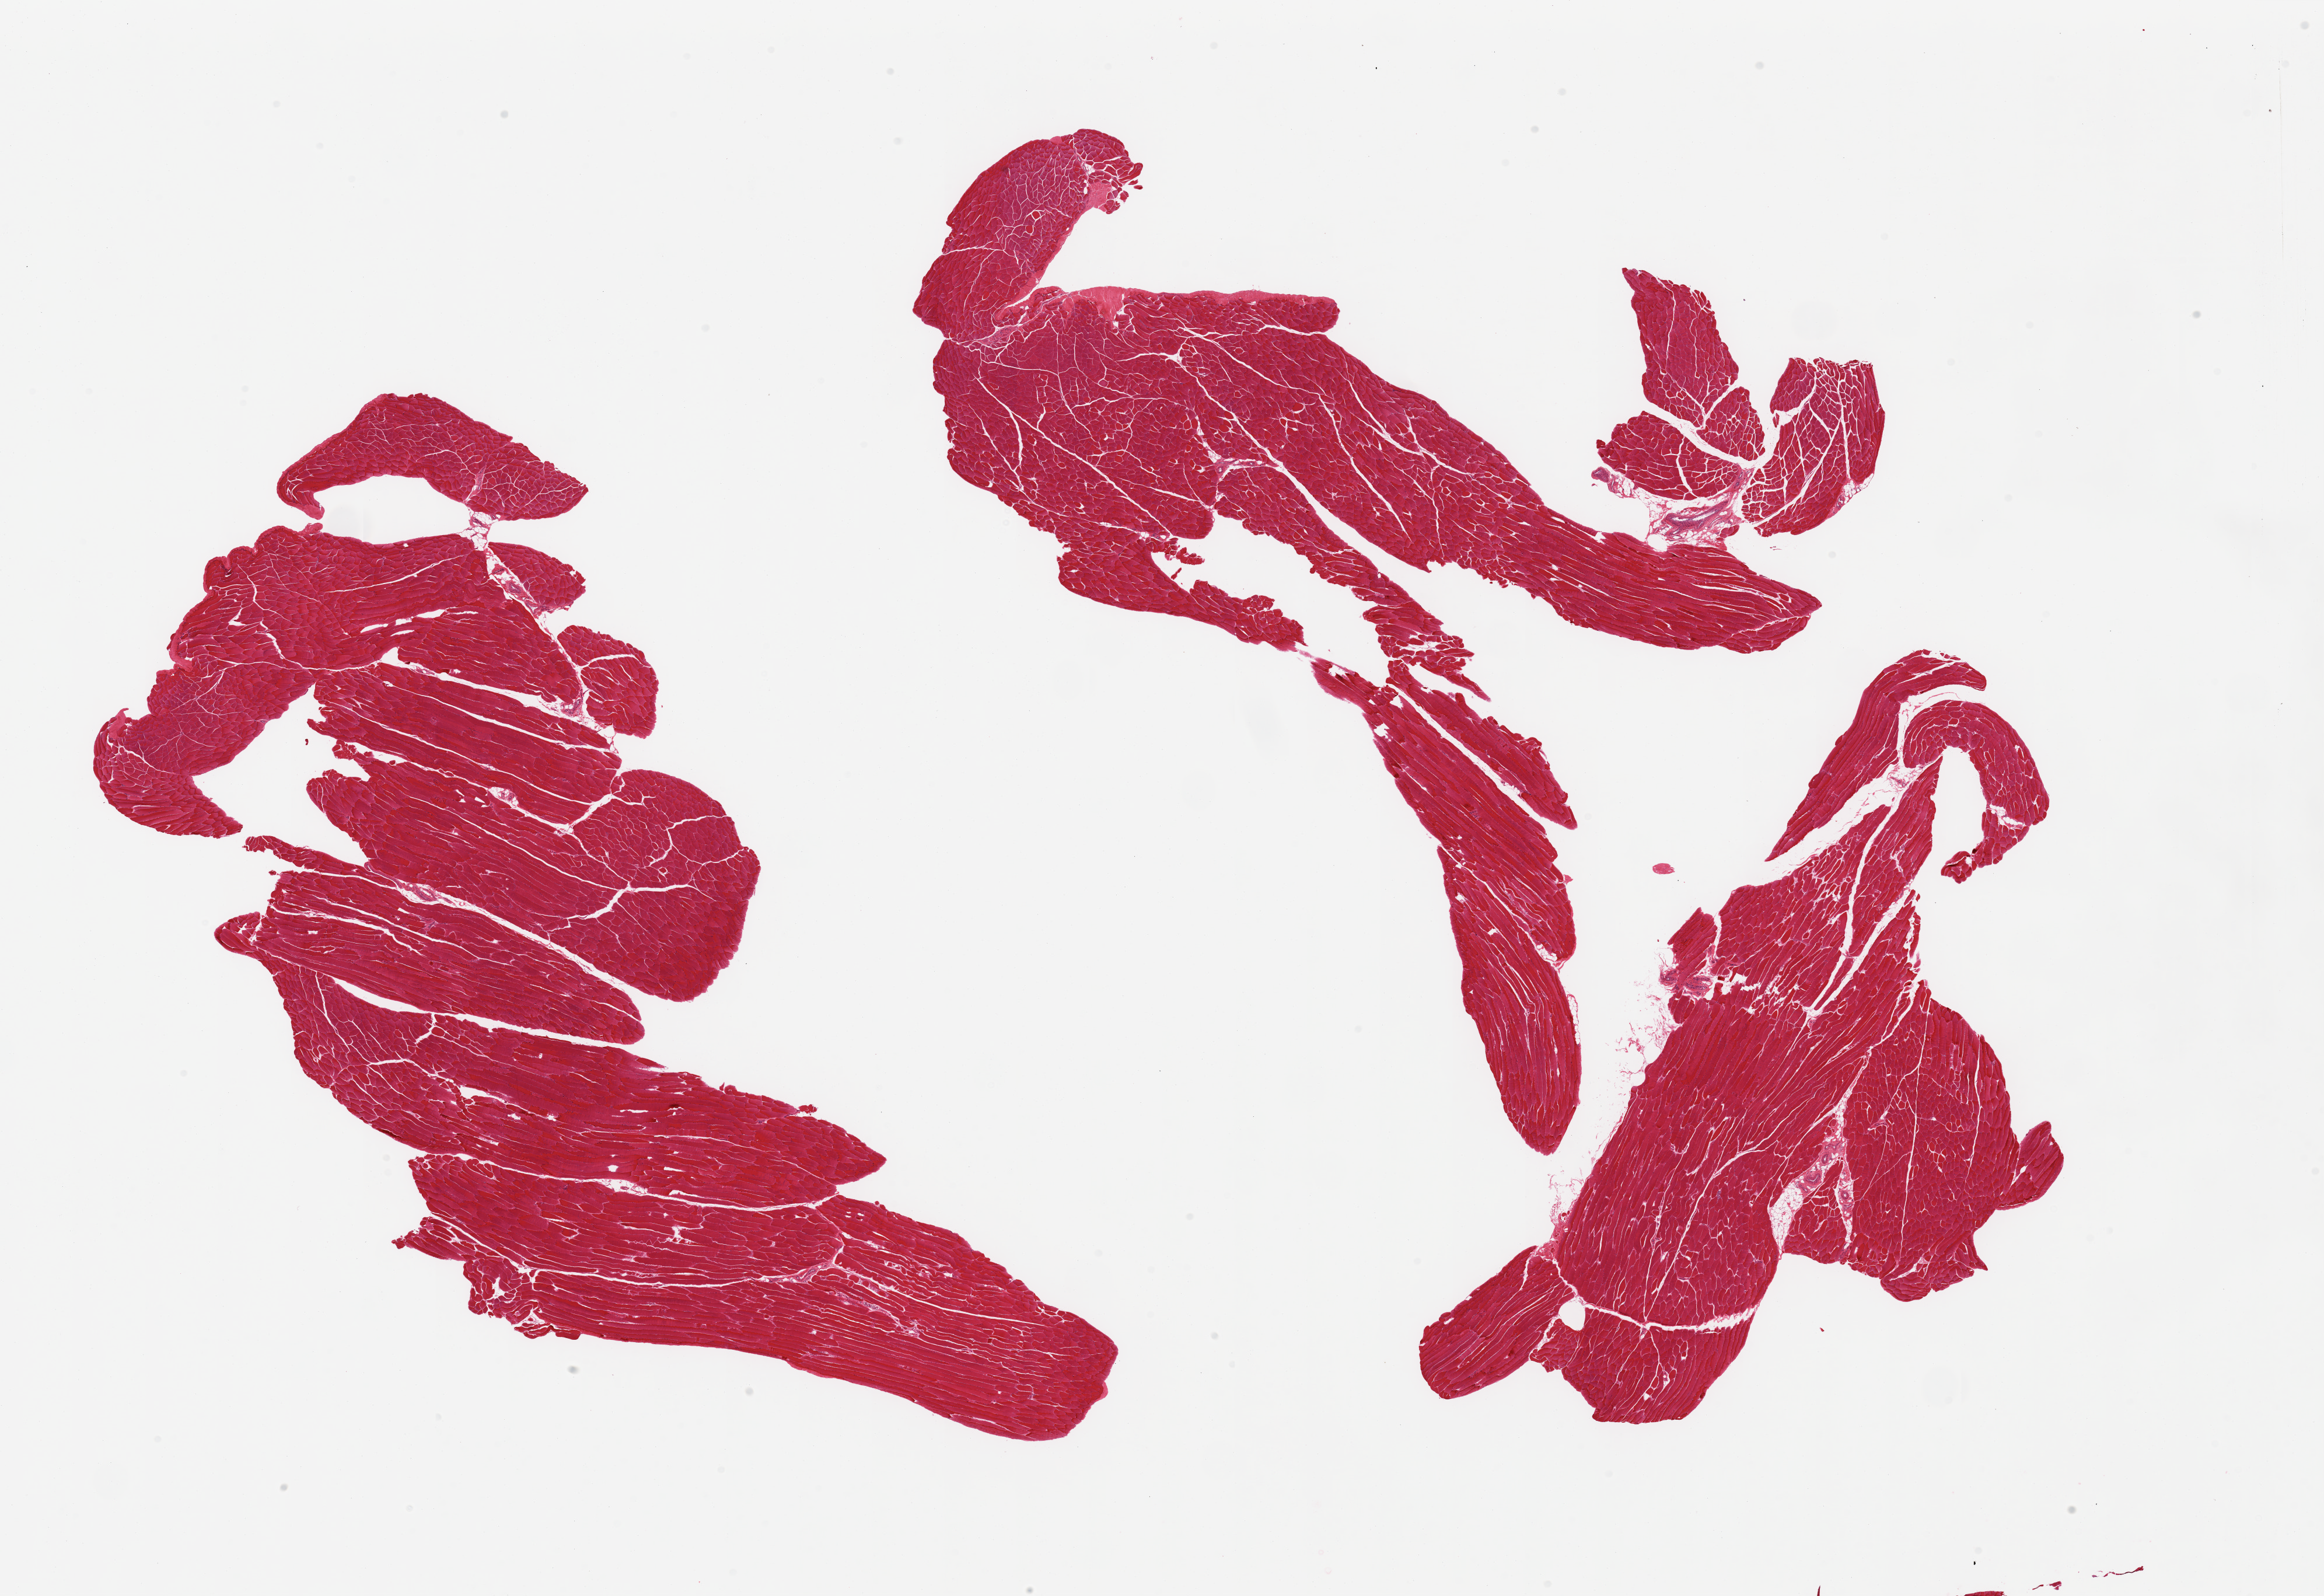
Whole-slide image, hematoxylin and eosin (H&E) stain, a low-resolution overview of the entire scanned area, about 31.5 x 21.6 mm (from a 20x scan); PAXgene-fixed paraffin-embedded (PFPE) section; section of skeletal muscle (target tissue); tissue donor sample. Donor: male.
- pathologist's review note for this sample: 2 pieces, trace interstitial fat